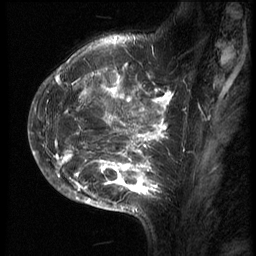
Breast MRI (dynamic contrast-enhanced), one sagittal slice. Position 23 of 70 along the scan axis. 3 images stored at this slice position (order not interpretable as contrast timing). 1.5 T. TE 4.2 ms, TR 9 ms. 2.5 mm slice thickness. 256 × 256 image matrix. Patient: female, 28 years. From the clinical record (not read from this slice): setting: breast cancer imaged before/during neoadjuvant chemotherapy.
Annotated regions visible in this slice (semi-automatic segmentation, software-assisted and operator-edited):
- analysis volume of interest (the breast-tissue region the enhancement analysis was run in; not a lesion): bounding box [x1, y1, x2, y2] px = [43, 42, 186, 215]
- tumour enhancement mask (voxels above the 140 % enhancement threshold inside the analysis volume of interest): [46, 54, 174, 210]